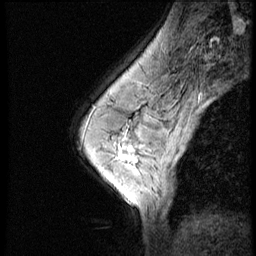
Breast MRI (dynamic contrast-enhanced), one sagittal slice. Position 37 of 52 along the scan axis. 3 images stored at this slice position (order not interpretable as contrast timing). 1.5 T. TE 4.2 ms, TR 9 ms. 2.5 mm slice thickness. 256 × 256 image matrix, field of view 180 × 180 mm. Patient: female, 50 years. From the clinical record (not read from this slice): setting: breast cancer imaged before/during neoadjuvant chemotherapy; receptor status: HR-positive, HER2-negative.
Outlined on this slice (semi-automatic segmentation, software-assisted and operator-edited):
- analysis volume of interest (the breast-tissue region the enhancement analysis was run in; not a lesion): bounding box <103,130,151,181> (left, top, right, bottom; pixels)
- tumour enhancement mask (voxels above the 140 % enhancement threshold inside the analysis volume of interest): <122,158,131,161>